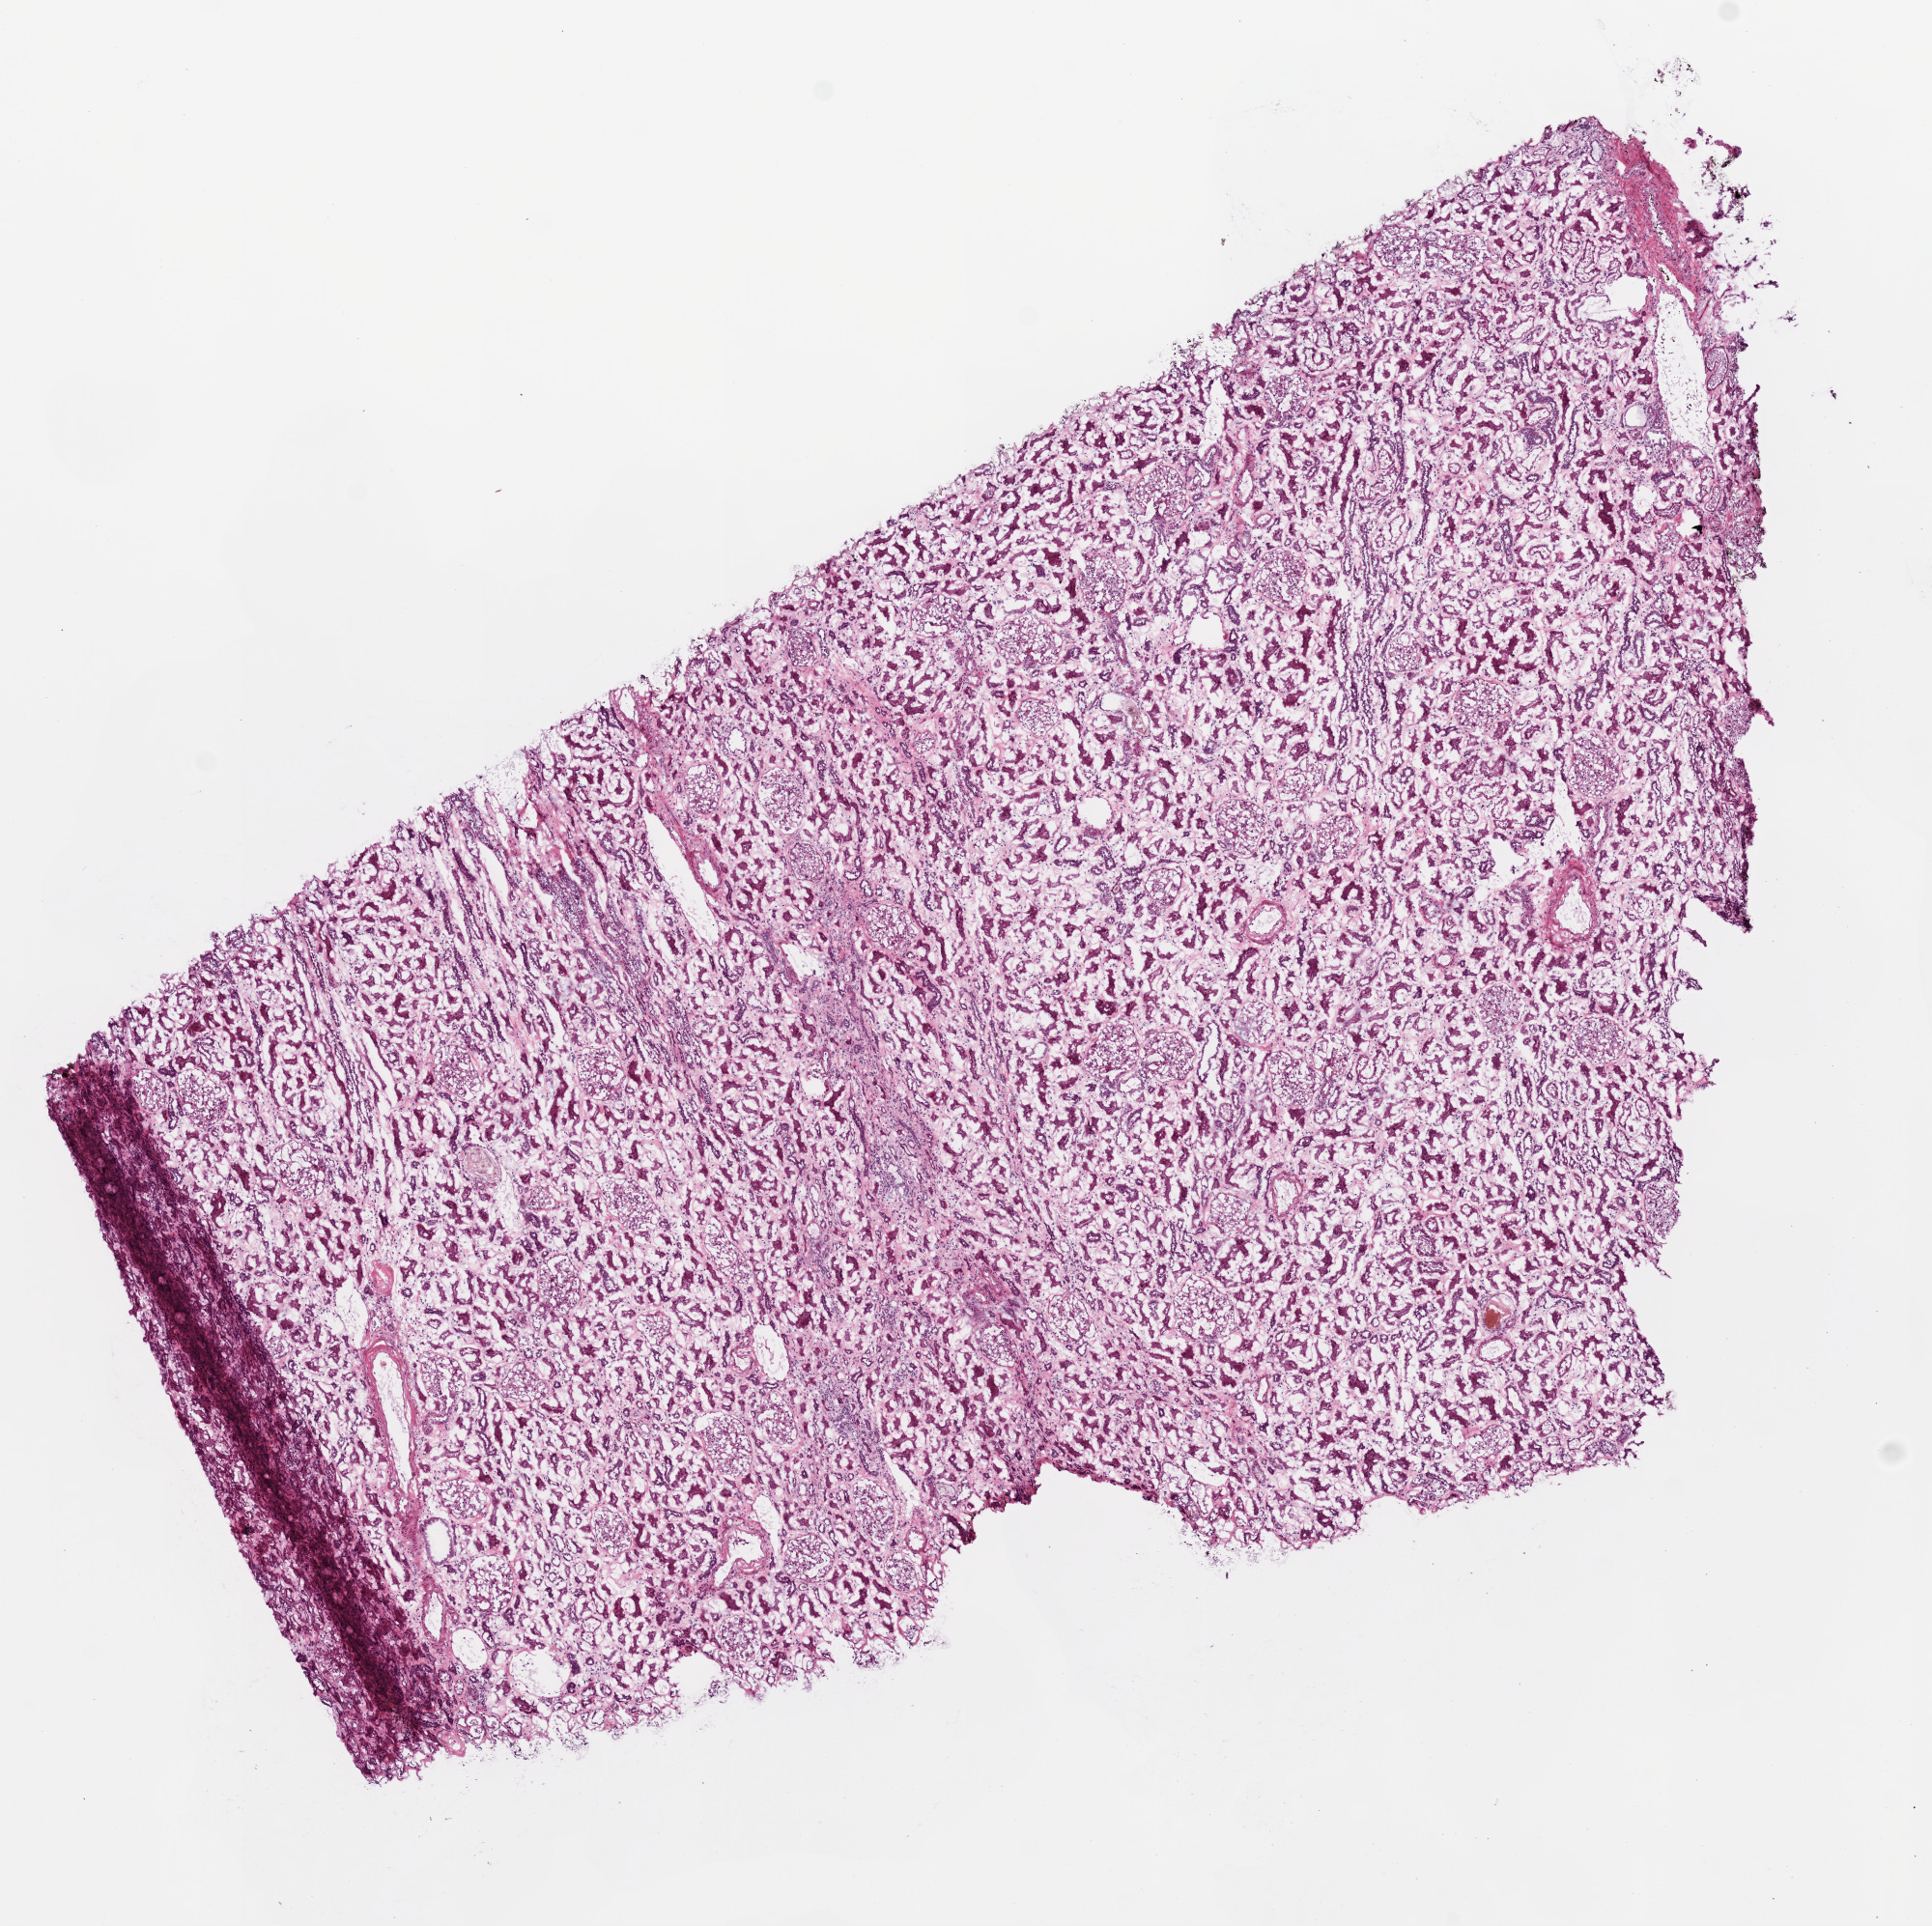
Digitized Hematoxylin and eosin (H&E) stained tissue section (whole slide), shown as a low-resolution overview of the whole scanned area (about 8.0 x 8.0 mm, slide scanned at 20x), frozen section, solid tissue normal (non-tumour tissue) sample from the kidney. Male patient; age at initial diagnosis 54 years.
This section: solid tissue normal (non-tumour) sample from the same patient. Patient diagnosis: Clear cell adenocarcinoma, NOS.